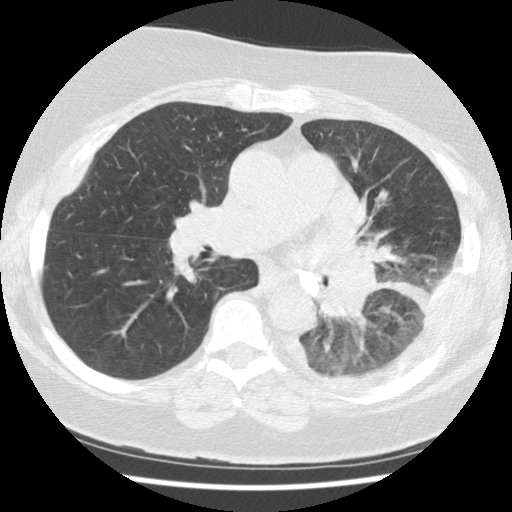
Axial slice from a low-dose chest CT screening exam. Baseline screening round. Lung window (W 1500 / L -600 HU). Standard (soft-tissue) reconstruction kernel (STANDARD). 120 kVp. Slice 53 of 114 in the series. 512 × 512 image matrix, field of view 320 × 320 mm. Female, age 65 years at enrolment. Current smoker at enrolment.
• Expert reader's lesion annotation, bounding box (x1, y1, x2, y2) in pixels: (296, 283, 392, 357).
• The exam's reader record, not a measurement of the box and not confirmed to be the same lesion: non-calcified nodule or mass ≥4 mm, left lower lobe, 74 × 48 mm, spiculated (stellate) margins, soft tissue attenuation.
• Later outcome: lung cancer diagnosed 13 days after this screen — adenocarcinoma, NOS, left lower lobe, stage IV (AJCC 6th edition), 74 mm at pathology.